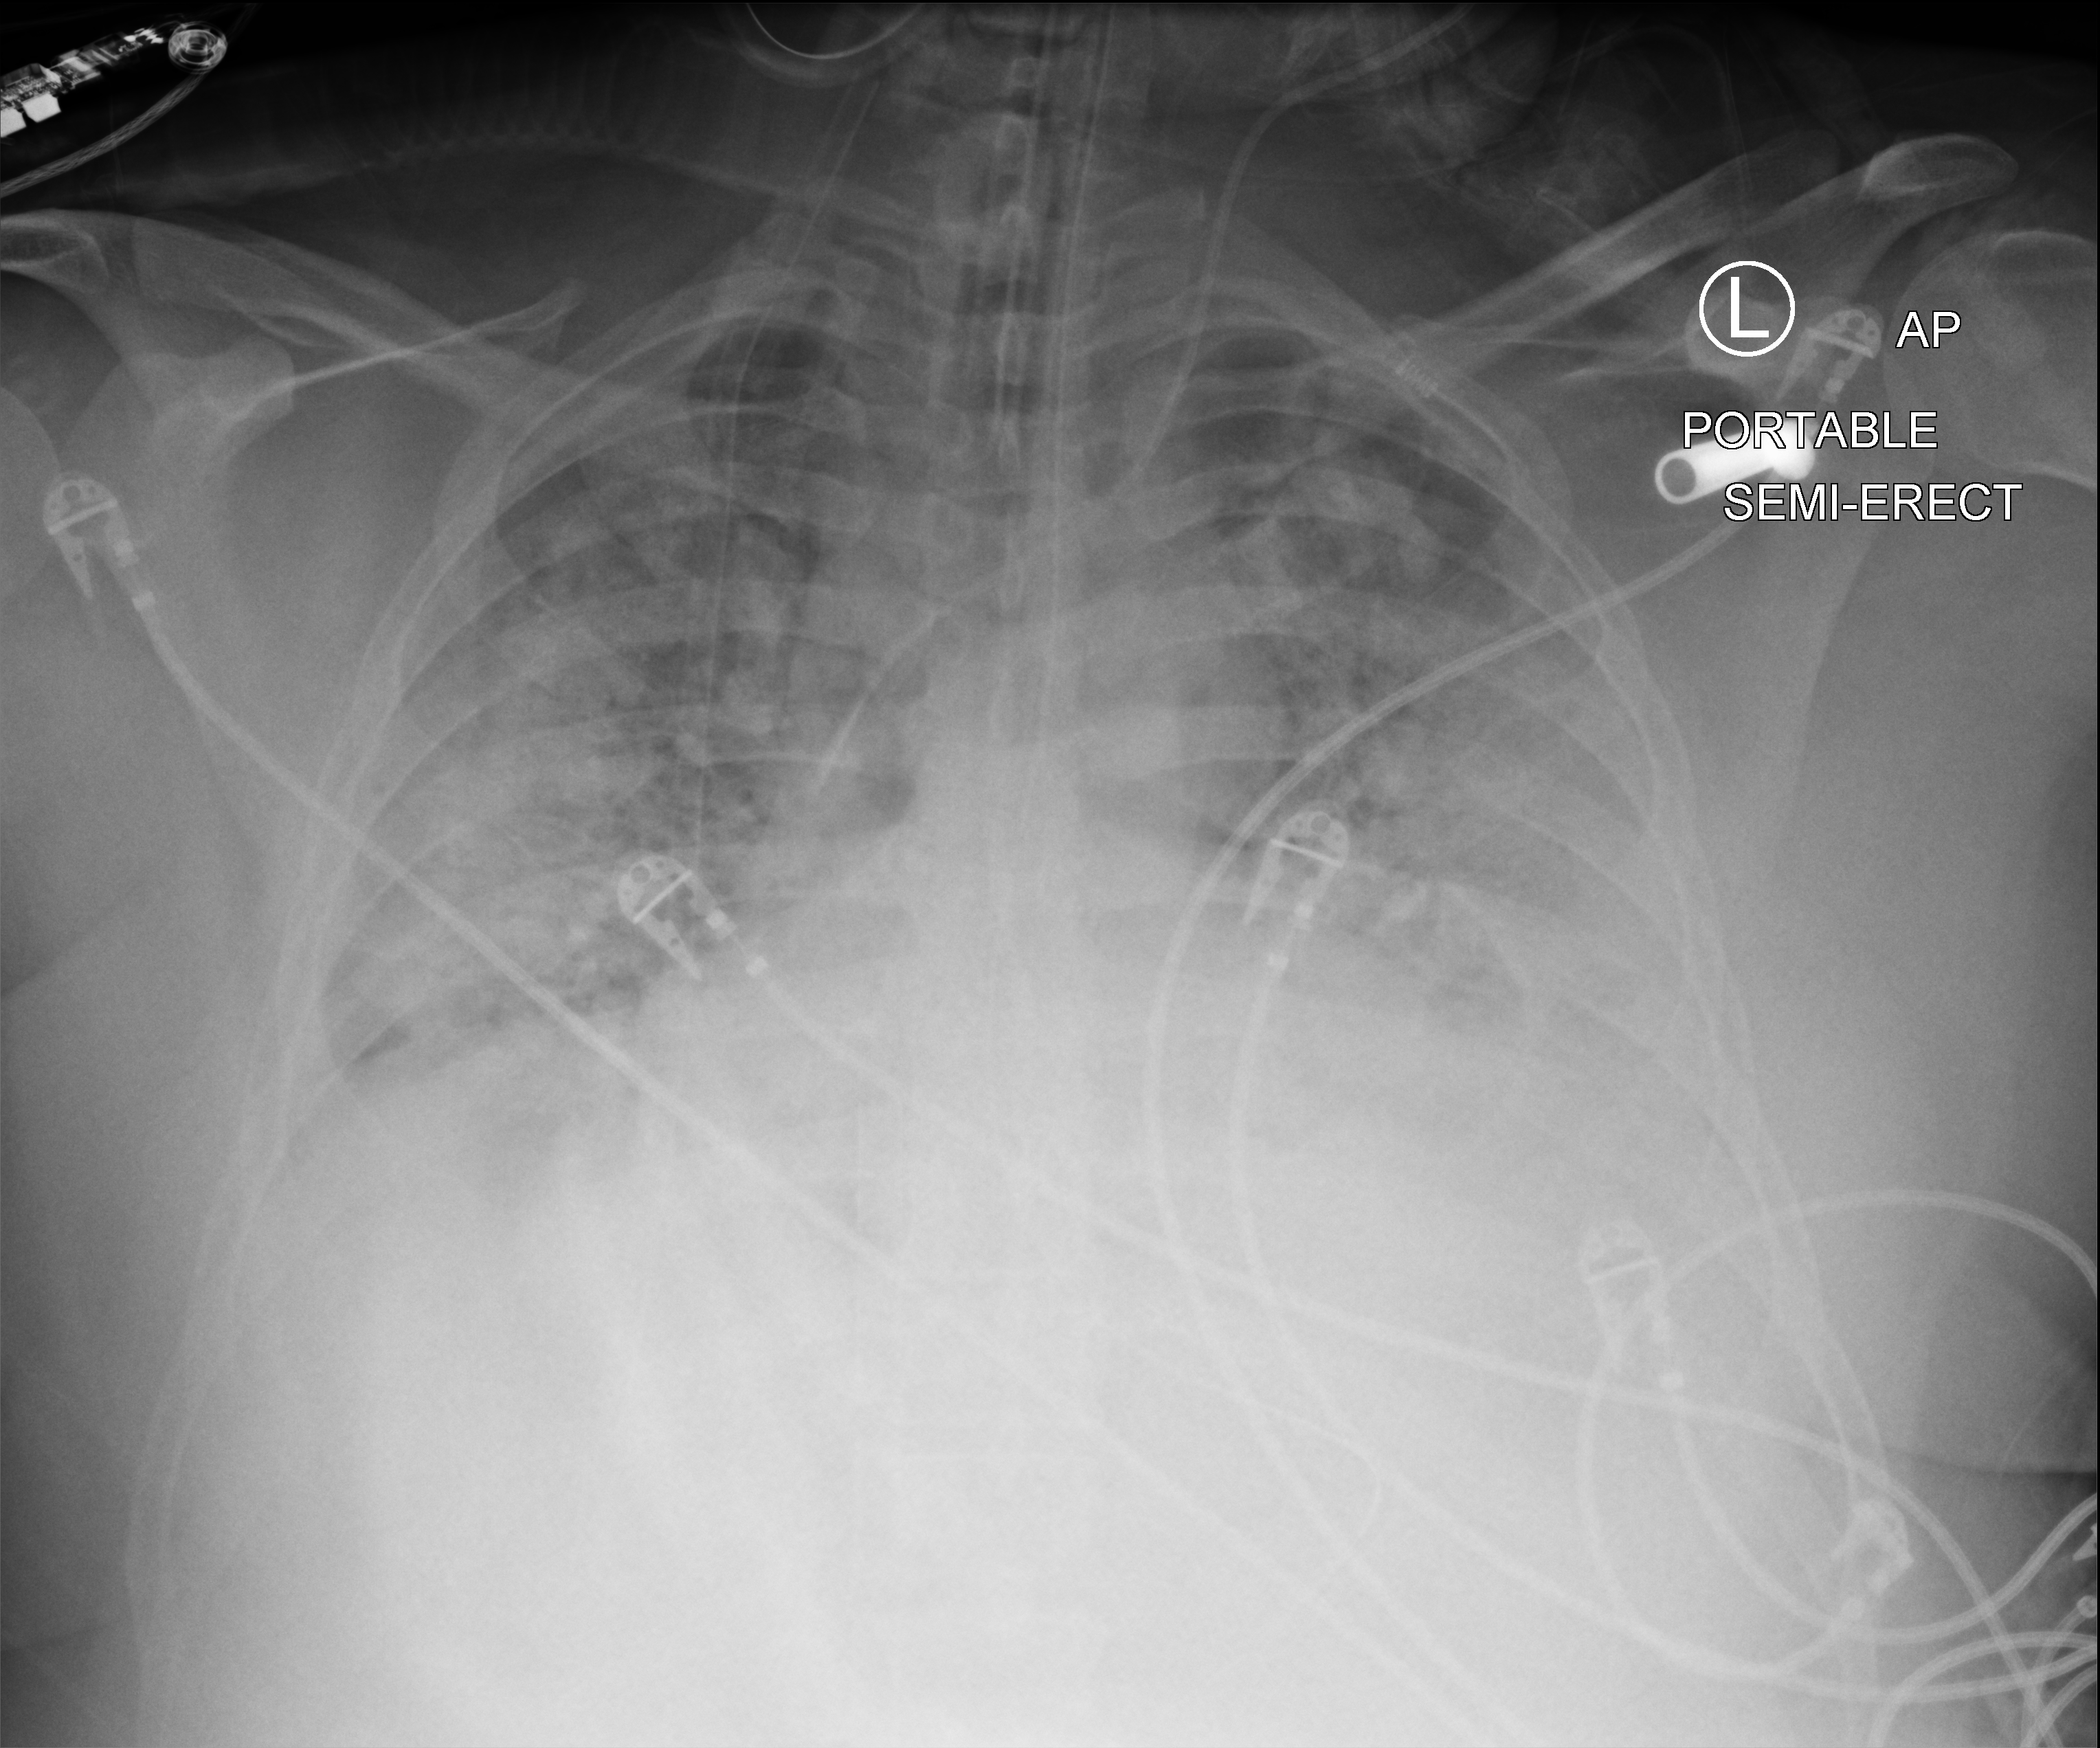
Chest X-ray (portable), anteroposterior (AP) projection. Adult patient hospitalised with COVID-19, age 18–59 years.
Hospital-stay facts (about this admission, not read from this image; timing relative to this image not recorded):
- admitted to intensive care during this hospital stay: yes
- mechanically ventilated during this hospital stay: yes